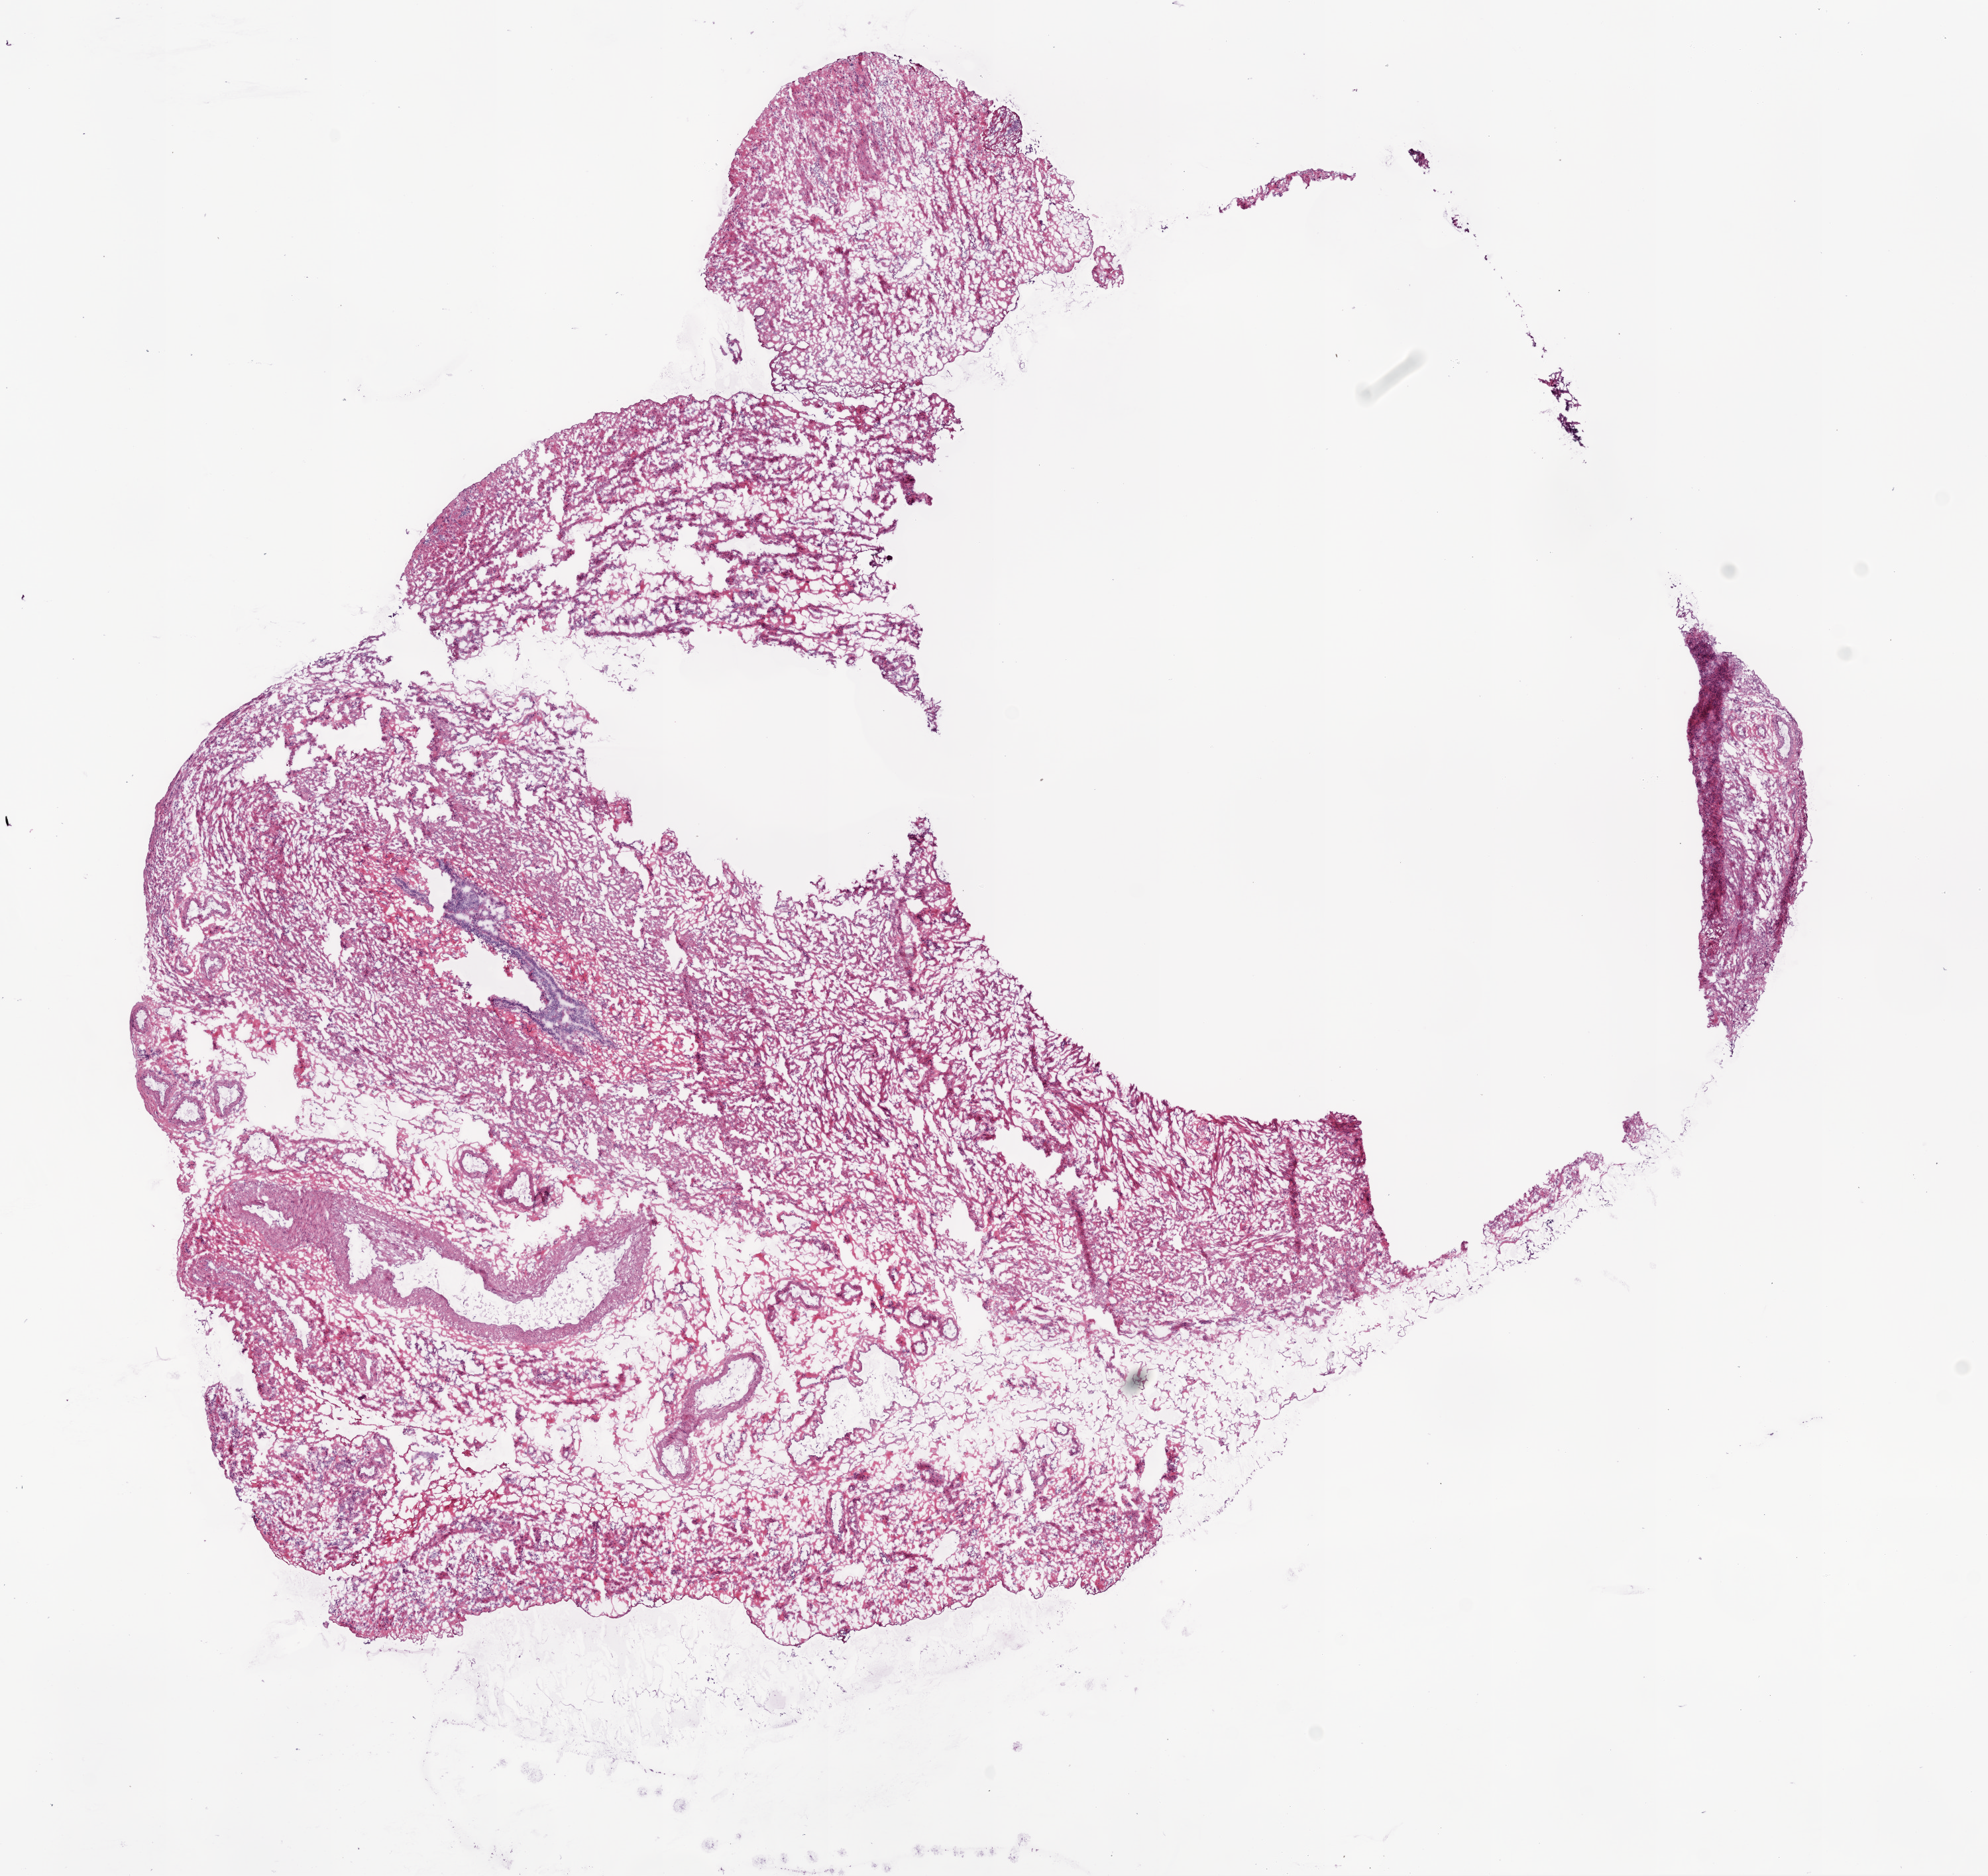
Hematoxylin and eosin (H&E) stained whole-slide image — low-resolution overview of the scanned area, about 12.0 x 11.4 mm; frozen section; sample: solid tissue normal (non-tumour tissue), ovary. Female, age 53 years at initial diagnosis.
This section: solid tissue normal (non-tumour) sample from the same patient. Patient diagnosis: Serous cystadenocarcinoma, NOS.